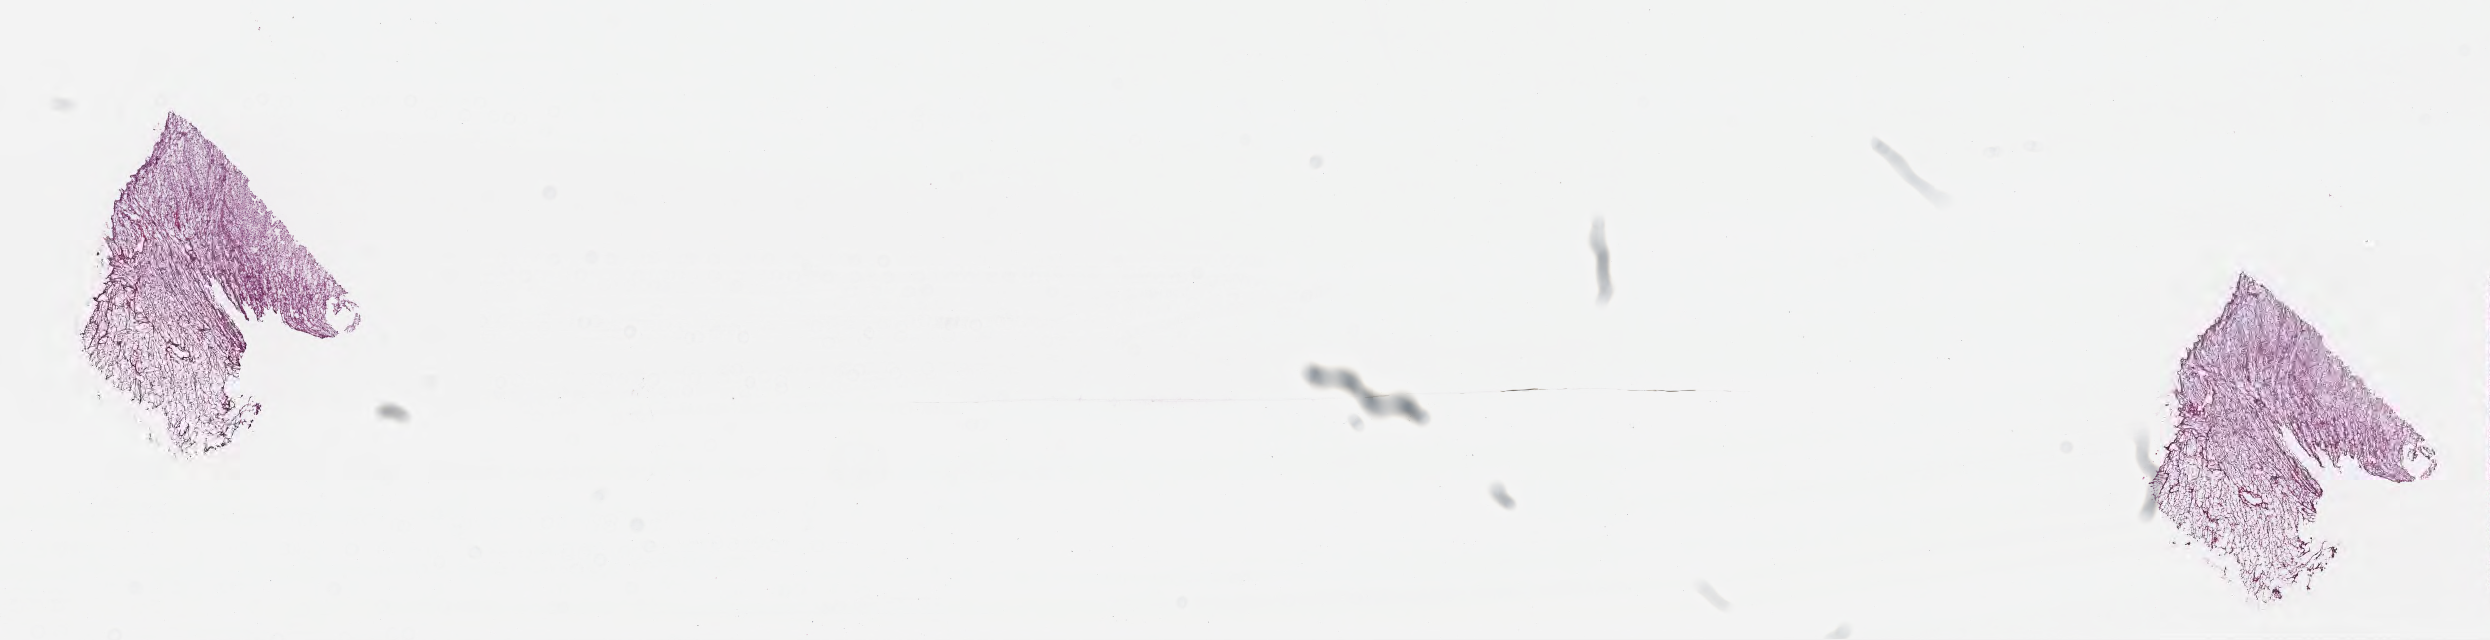
Hematoxylin and eosin (H&E) whole-slide image, low-resolution overview of the scanned area, about 20.1 x 5.2 mm, cryosection, primary tumor, site: soft tissue. Patient: female, age at initial diagnosis 25 years. Composition of this section per pathologist review: tumor cells 80%, tumor nuclei 90%, stromal cells 20%, necrosis 0%, normal cells 0%. Infiltration values recorded for this section: lymphocyte infiltration 0%, monocyte infiltration 0%, neutrophil infiltration 0%.
Section: bottom of the tissue portion. Diagnosis: Spindle cell sarcoma.